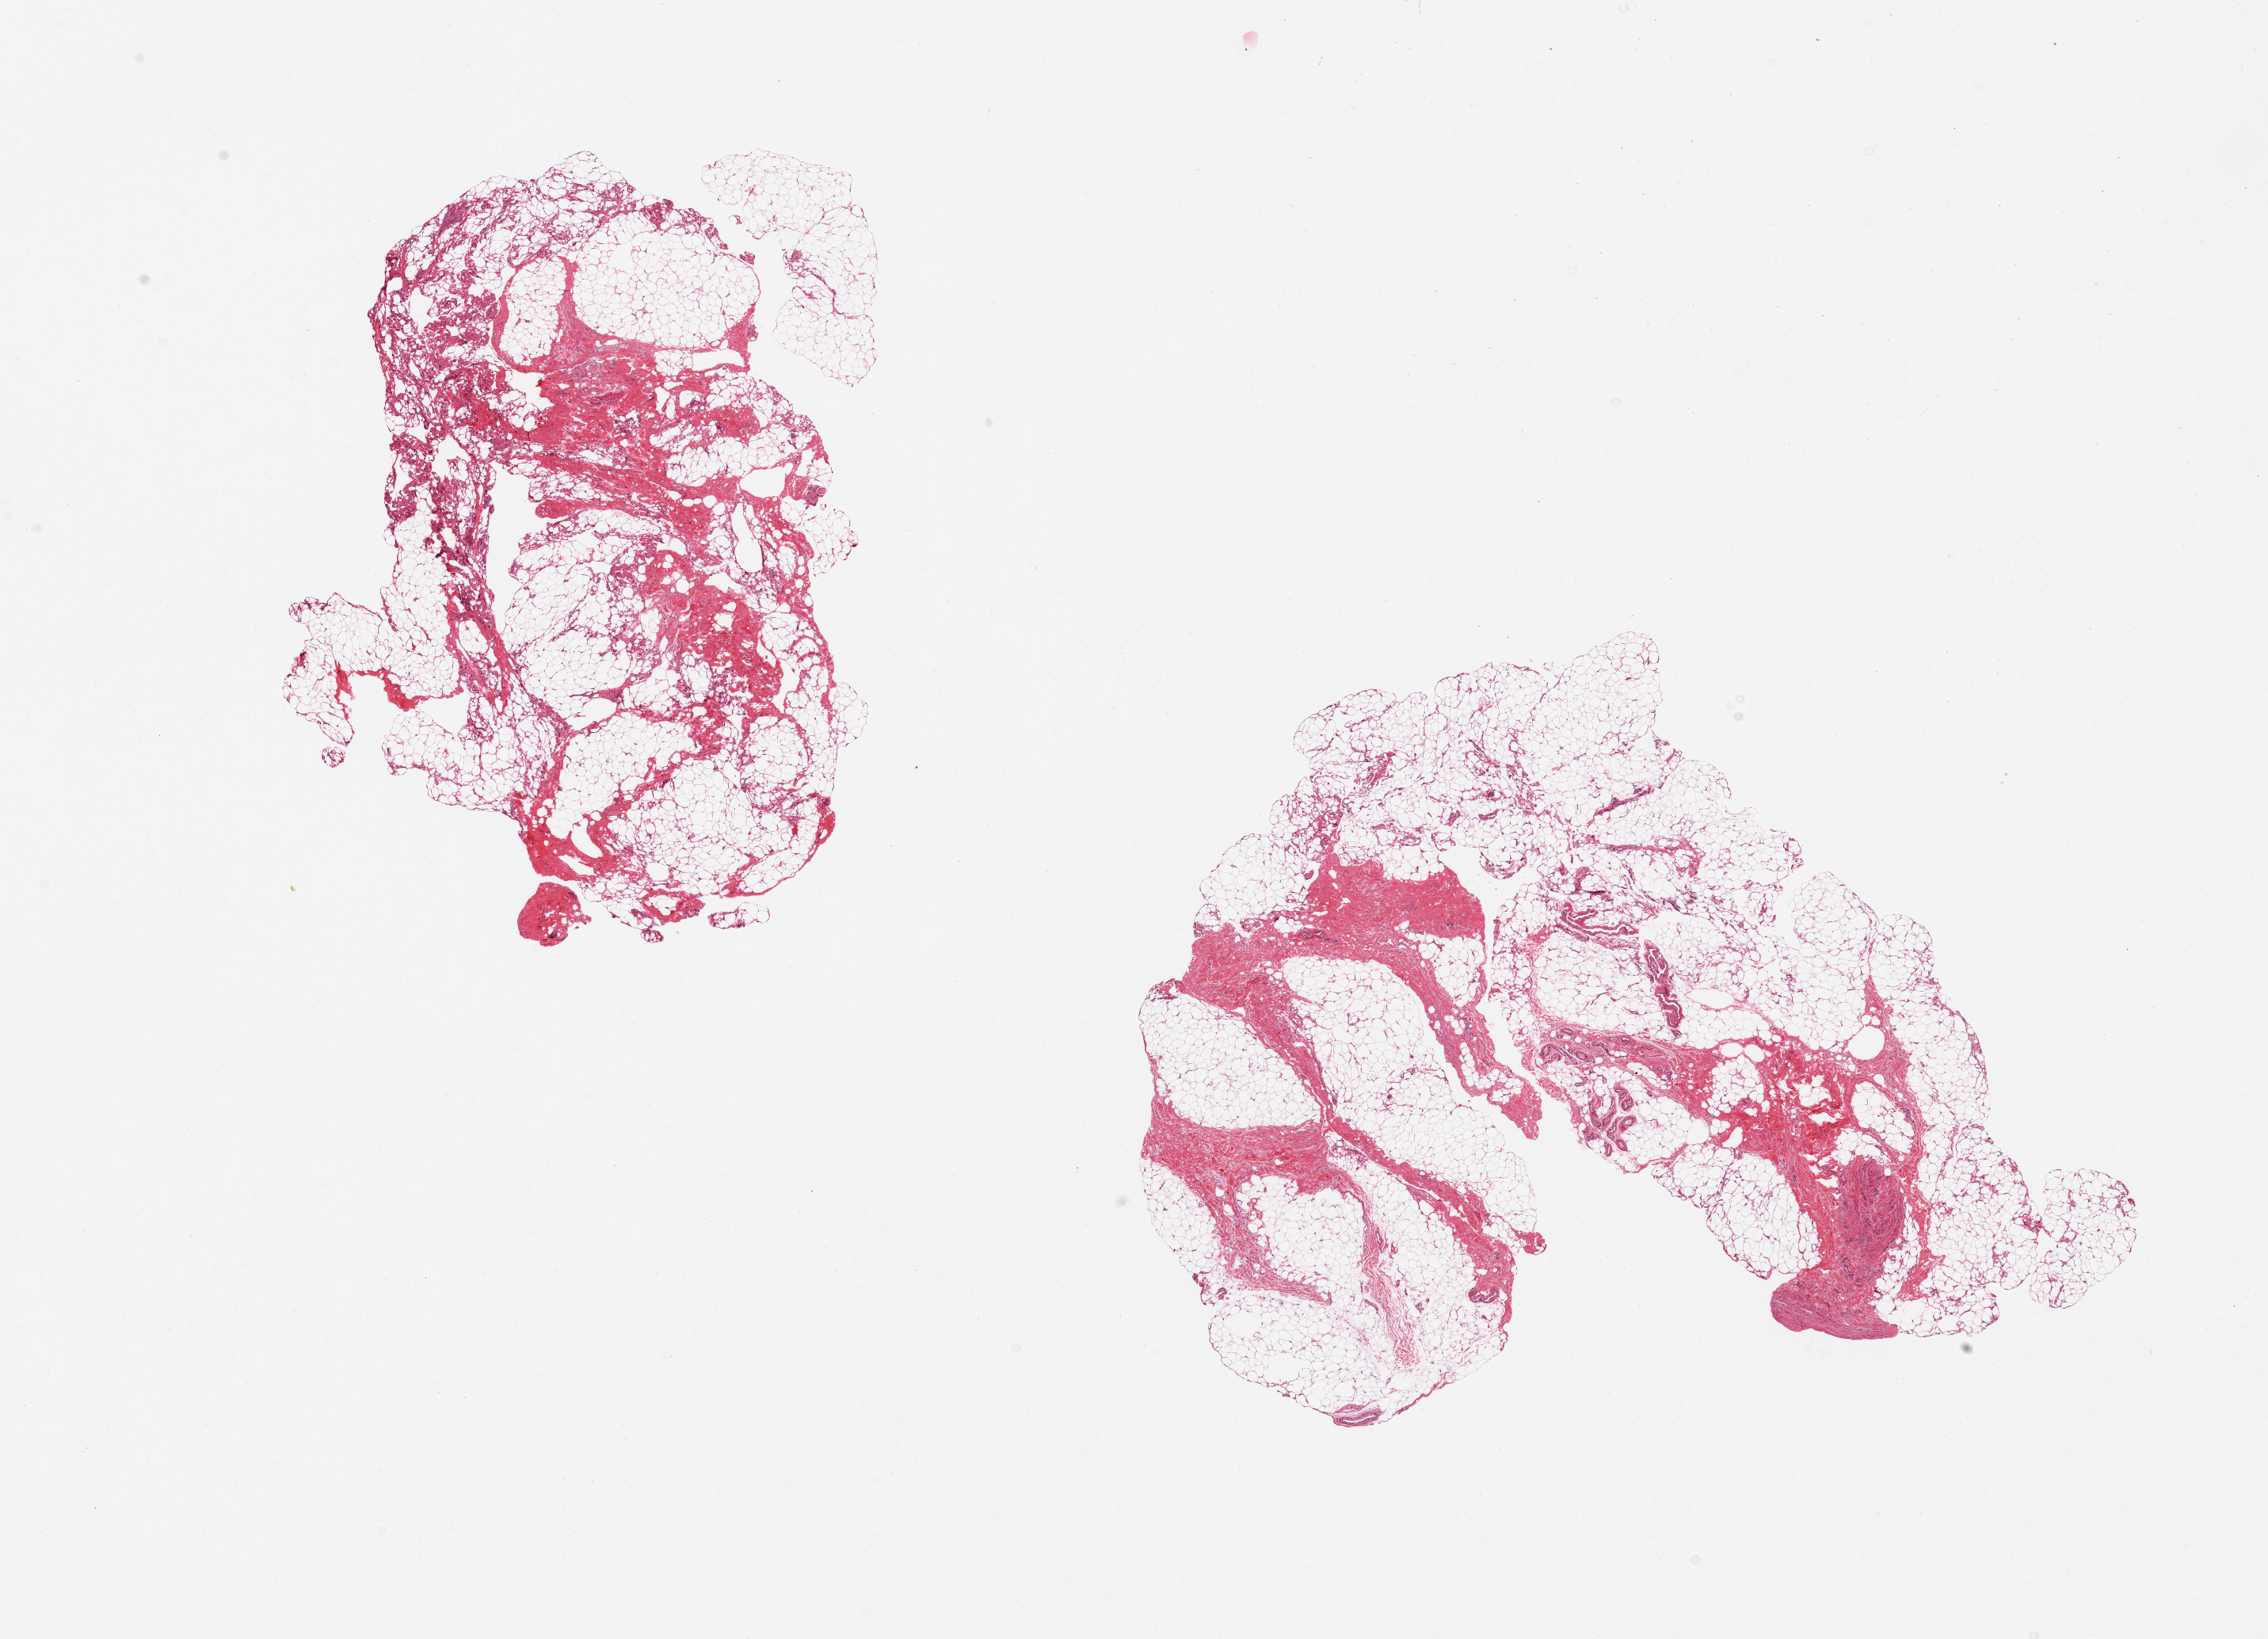
Whole-slide image, H&E stain — a low-resolution overview of the entire scanned area, about 22.6 x 16.4 mm (acquisition: 20x scan). PAXgene-fixed paraffin-embedded (PFPE) section. Section of adipose tissue (target tissue). Tissue donor sample. Female donor.
Reviewer comment on this tissue sample: 2 pieces, 30-40% fibrovascular tissue.